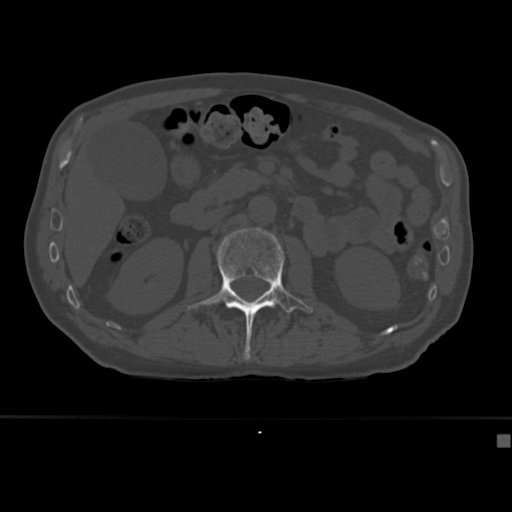
CT including the spine, one axial slice. Slice 149 of 430 in the series (ordered by position). Reconstruction kernel Br40s. Bone window (W 1800 / L 400 HU). 1.5 mm slice thickness. 512 × 512 image matrix, field of view 337 × 337 mm. Patient: male, 64 years. From the clinical record (not read from this slice): primary cancer: uterus; vertebrae with lytic lesions (as recorded): T1, T4, T5, T7, L5.
Structures marked on this image (semi-automatic segmentation, software-assisted and operator-edited):
- L2 vertebra: bounding box <187,228,313,360> (left, top, right, bottom; pixels)